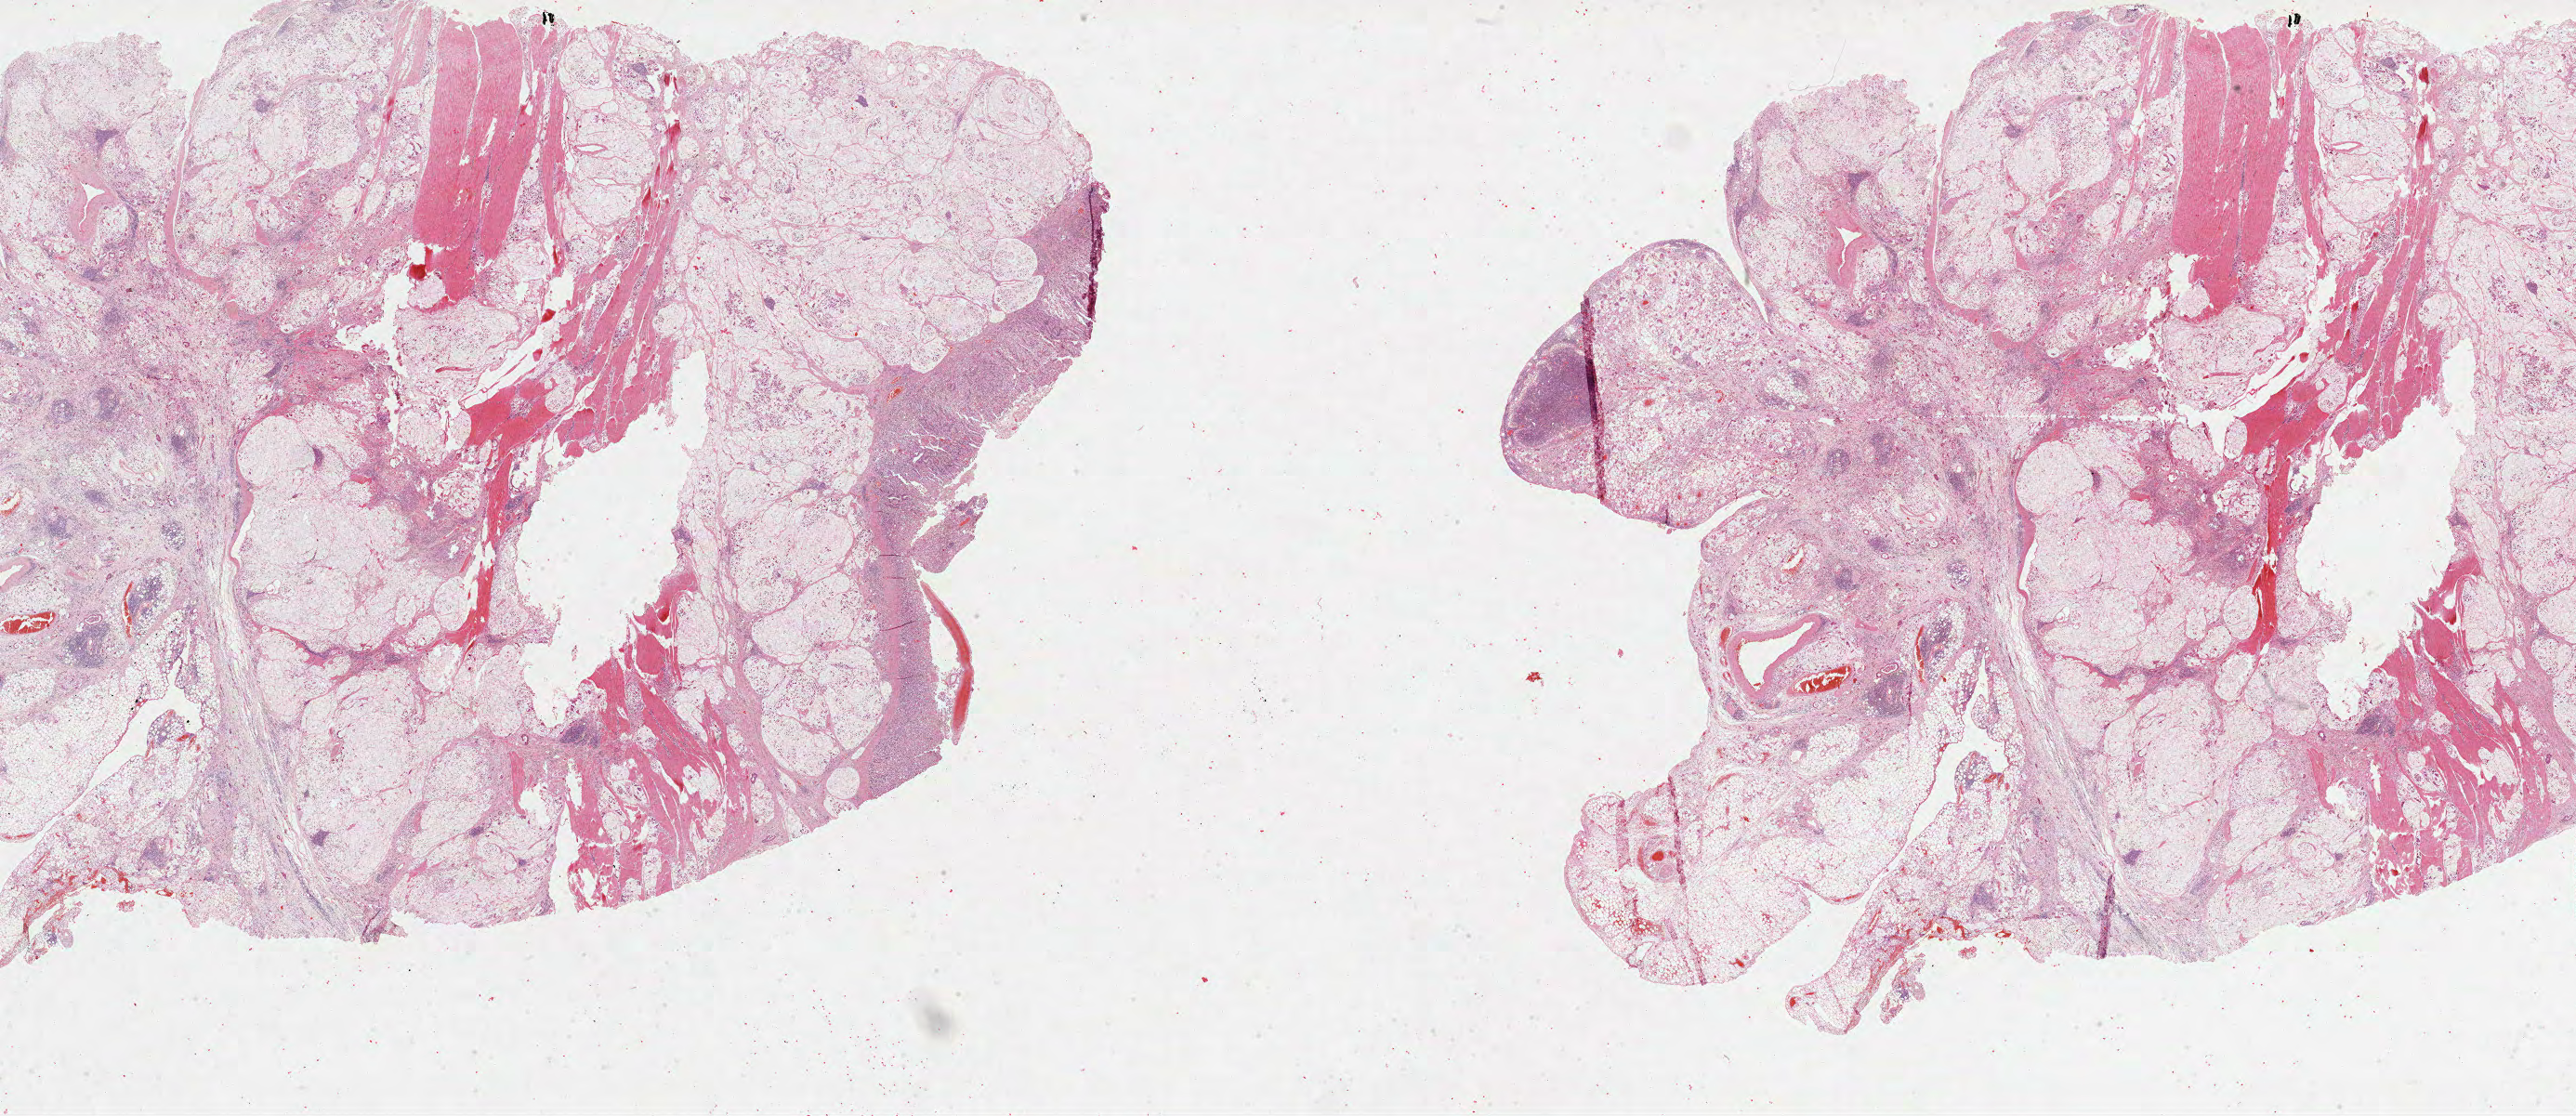
Digitized H&E-stained tissue section (whole slide) — shown as a low-resolution overview of the whole scanned area (about 44.7 x 19.4 mm, from a 40x scan). Formalin-fixed paraffin-embedded (FFPE) diagnostic section. Primary tumour sample from the stomach. Male, age 74 years at initial diagnosis. Histologic grade: G3 (poorly differentiated).
TNM: T3 N2 M0. AJCC pathologic stage: IIIA (7th edition). Diagnosis: Mucinous adenocarcinoma (body of stomach).